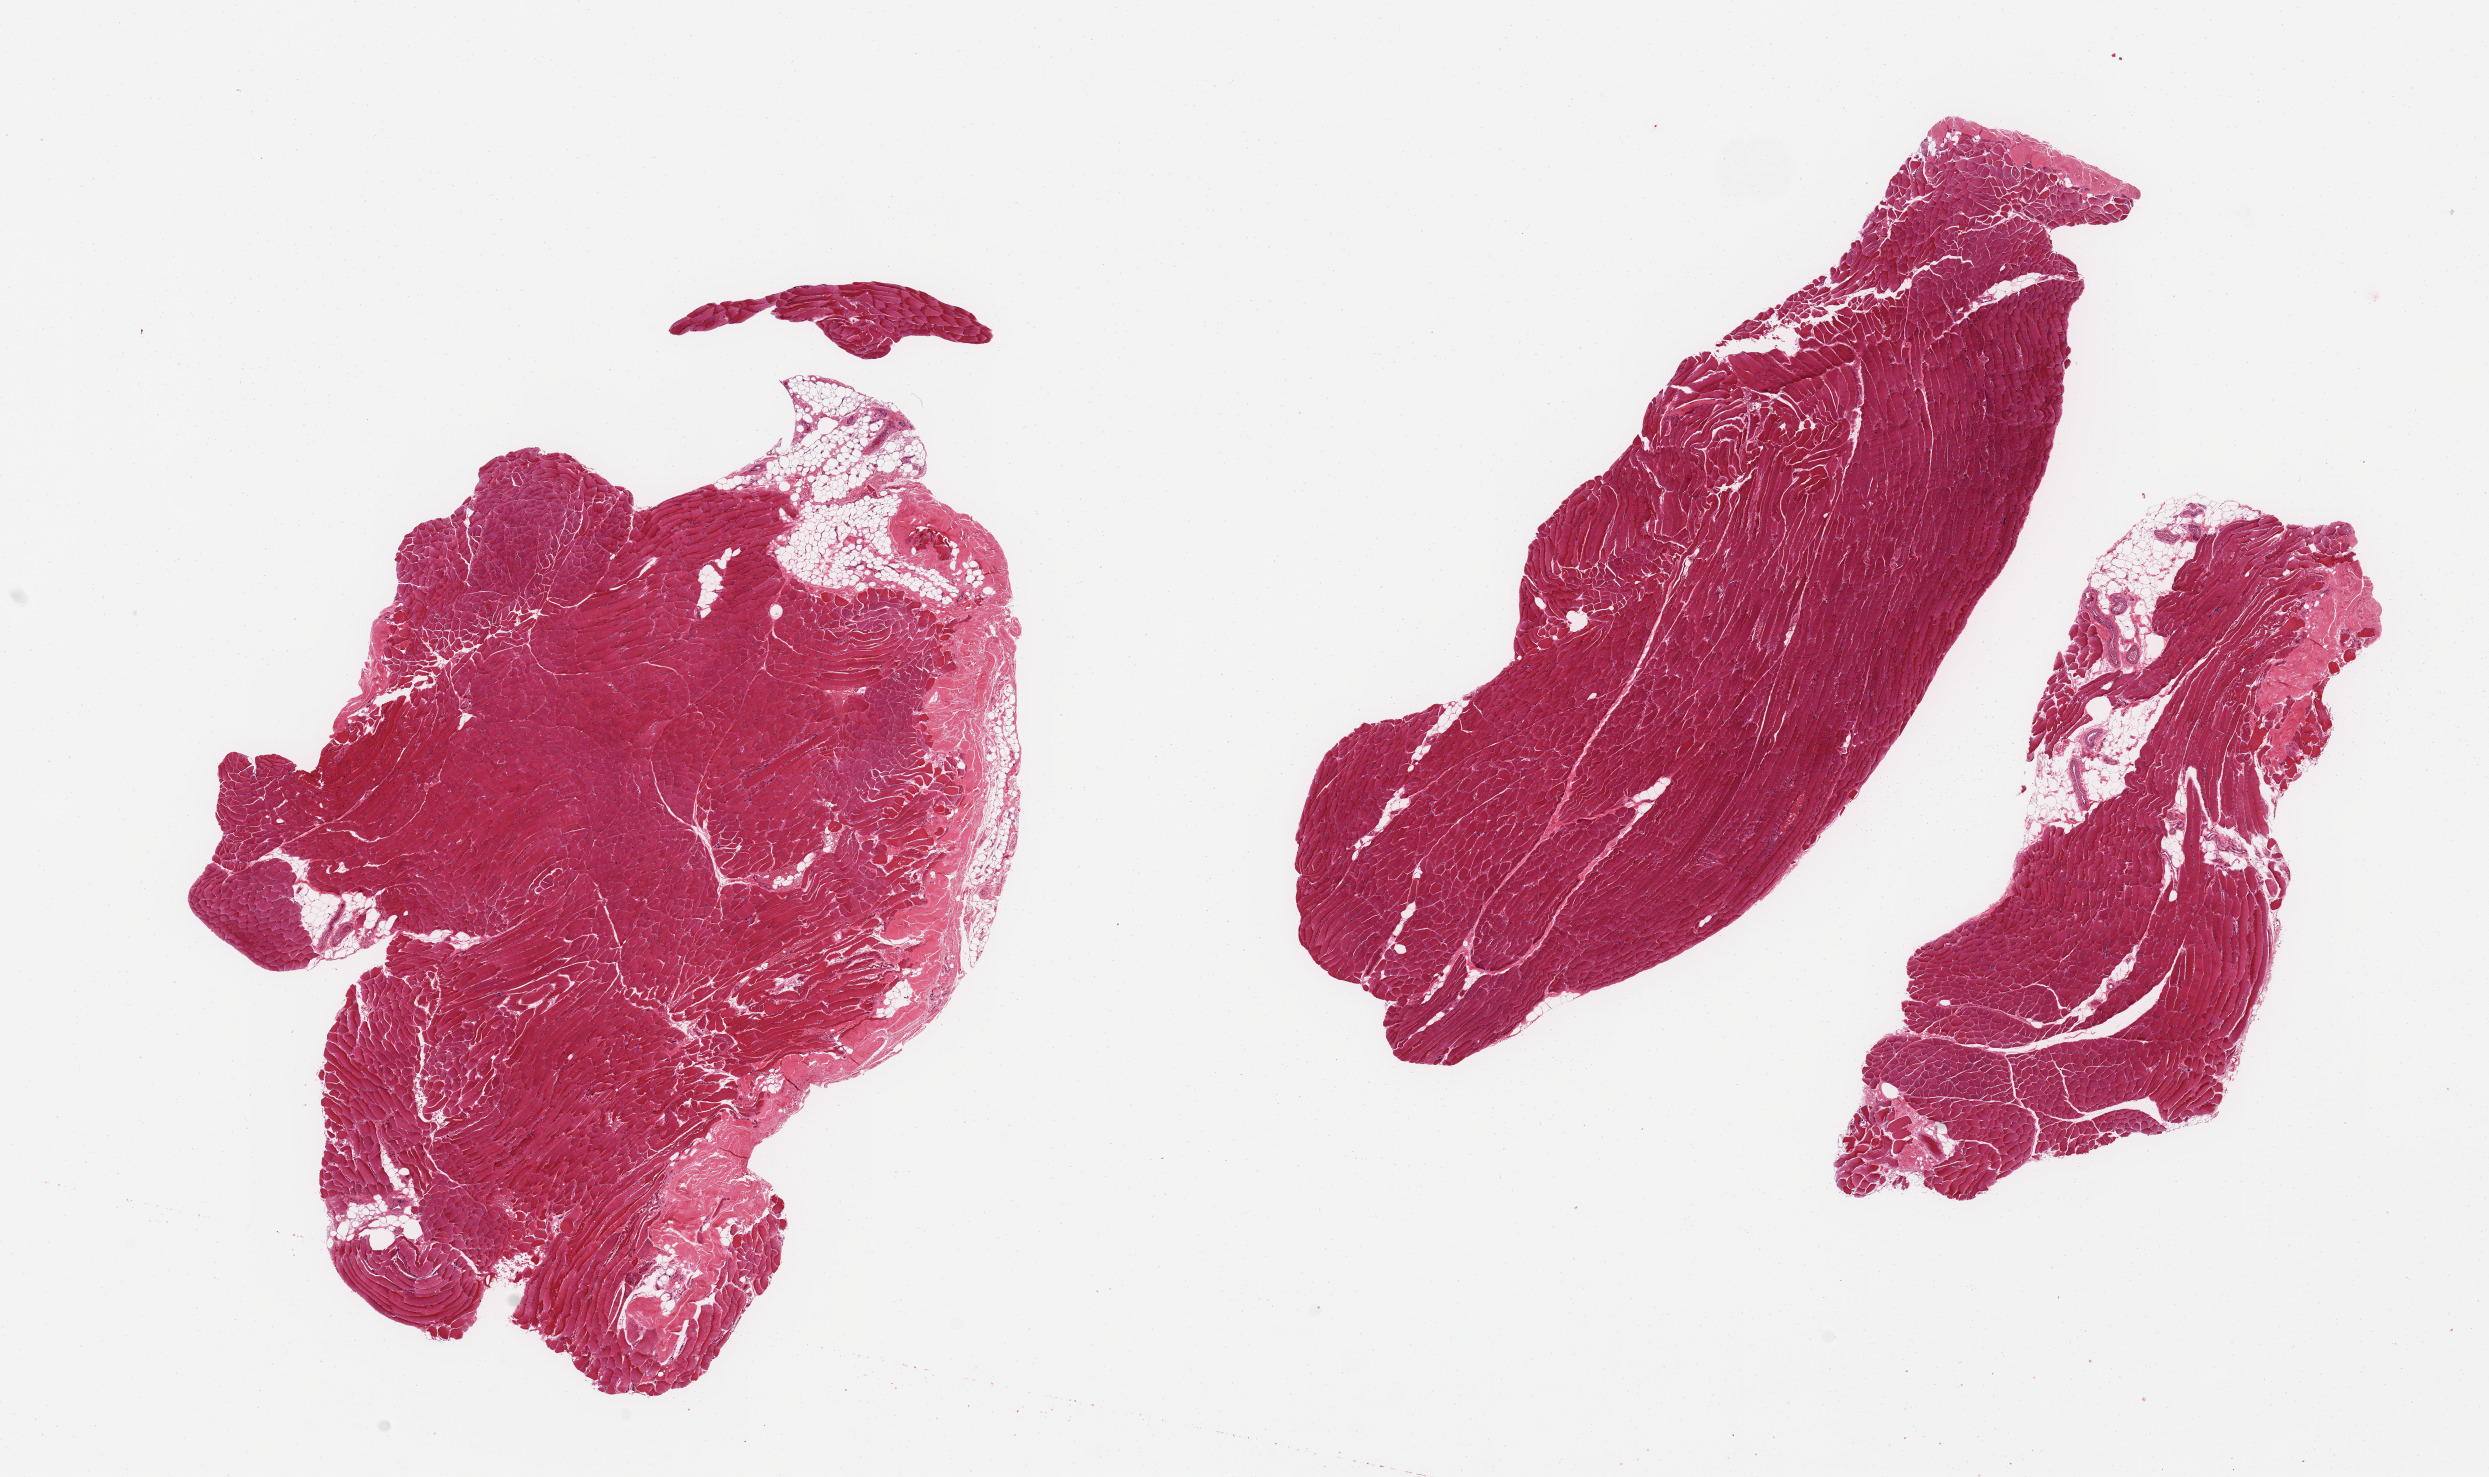
Digitized hematoxylin and eosin (H&E)-stained section, a low-resolution overview of the entire scanned area, about 19.7 x 11.7 mm (acquisition: 20x scan), PAXgene-fixed paraffin-embedded (PFPE) section, target tissue: skeletal muscle, tissue donor sample. Donor: male.
Reviewer comment on this tissue sample: 3 pieces; 10, 5, & 2% fibrofatty content.